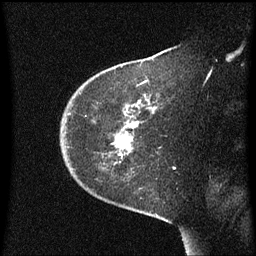
Breast MRI (dynamic contrast-enhanced), one sagittal slice. Position 46 of 60 along the scan axis. Dynamic contrast-enhanced series, image 2 of 3 at this slice position (ordered by acquisition). 1.5 T. TE 4.2 ms, TR 8.4 ms. 2 mm slice thickness. 256 × 256 image matrix, field of view 200 × 200 mm. Female patient, age 38 years. From the clinical record (not read from this slice): setting: breast cancer imaged before/during neoadjuvant chemotherapy; receptor status: HER2-positive.
Structures marked on this image (semi-automatic segmentation, software-assisted and operator-edited):
- analysis volume of interest (the breast-tissue region the enhancement analysis was run in; not a lesion): box from (x=61, y=50) to (x=171, y=185) px
- tumour enhancement mask (voxels above the 70 % enhancement threshold inside the analysis volume of interest): (x=121, y=154)–(x=123, y=157)